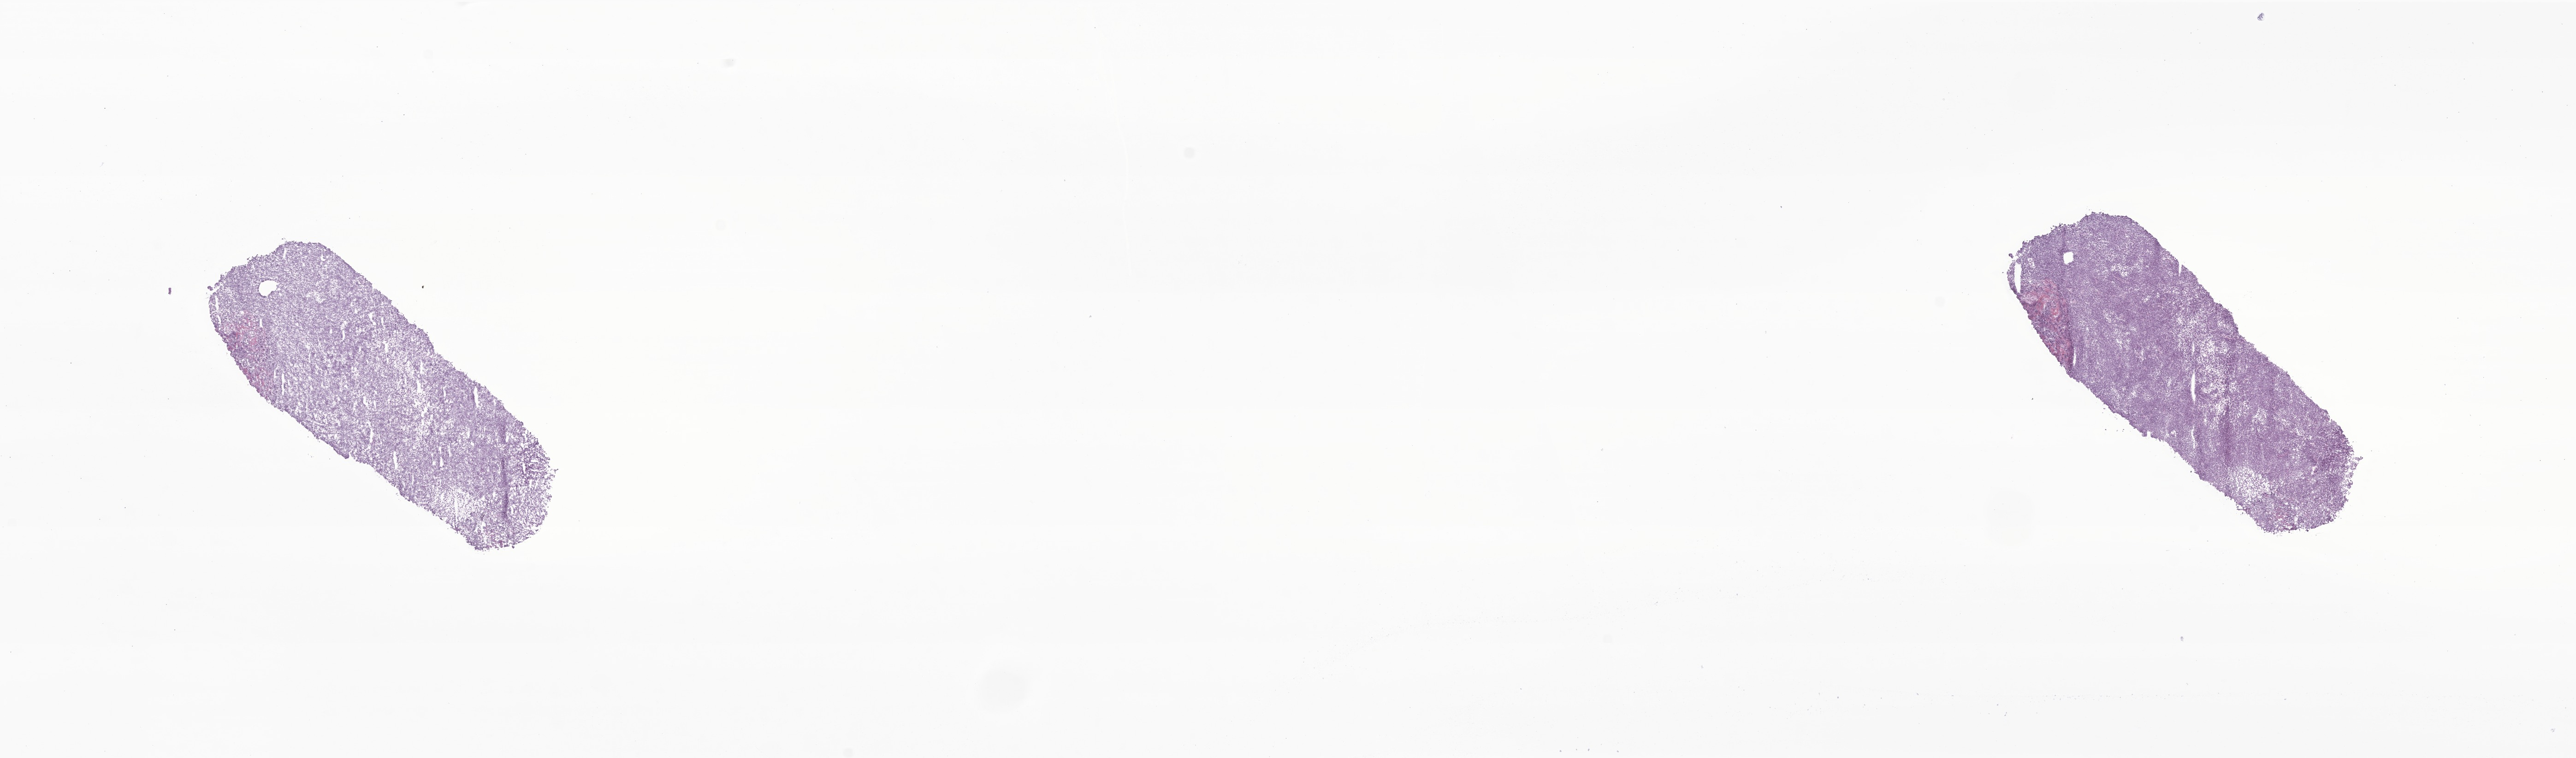
Whole-slide image, hematoxylin and eosin (H&E) stain of tumor tissue from the pineal gland, whole scanned area (about 23.6 x 6.9 mm) shown as a low-resolution overview, frozen section. Male patient, age 74 months.
Diagnosis: Pineoblastoma.